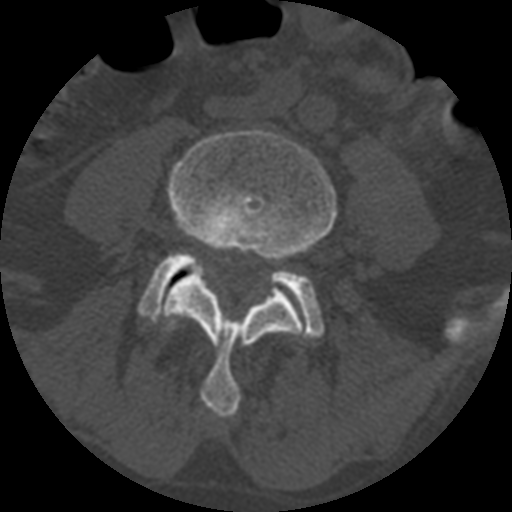
CT including the spine, one axial slice; slice 273 of 399 in the series (ordered by position); reconstruction kernel STANDARD; bone window (W 1800 / L 400 HU); 1.25 mm slice thickness; 512 × 512 image matrix, field of view 160 × 160 mm. Patient age 71 years. Case-level facts recorded for this patient, not image findings: primary cancer: prostate.
Annotated regions visible in this slice (semi-automatically segmented with operator editing):
- L4 vertebra: box from (x=157, y=129) to (x=338, y=418) px
- L5 vertebra: (x=138, y=252)–(x=324, y=338)